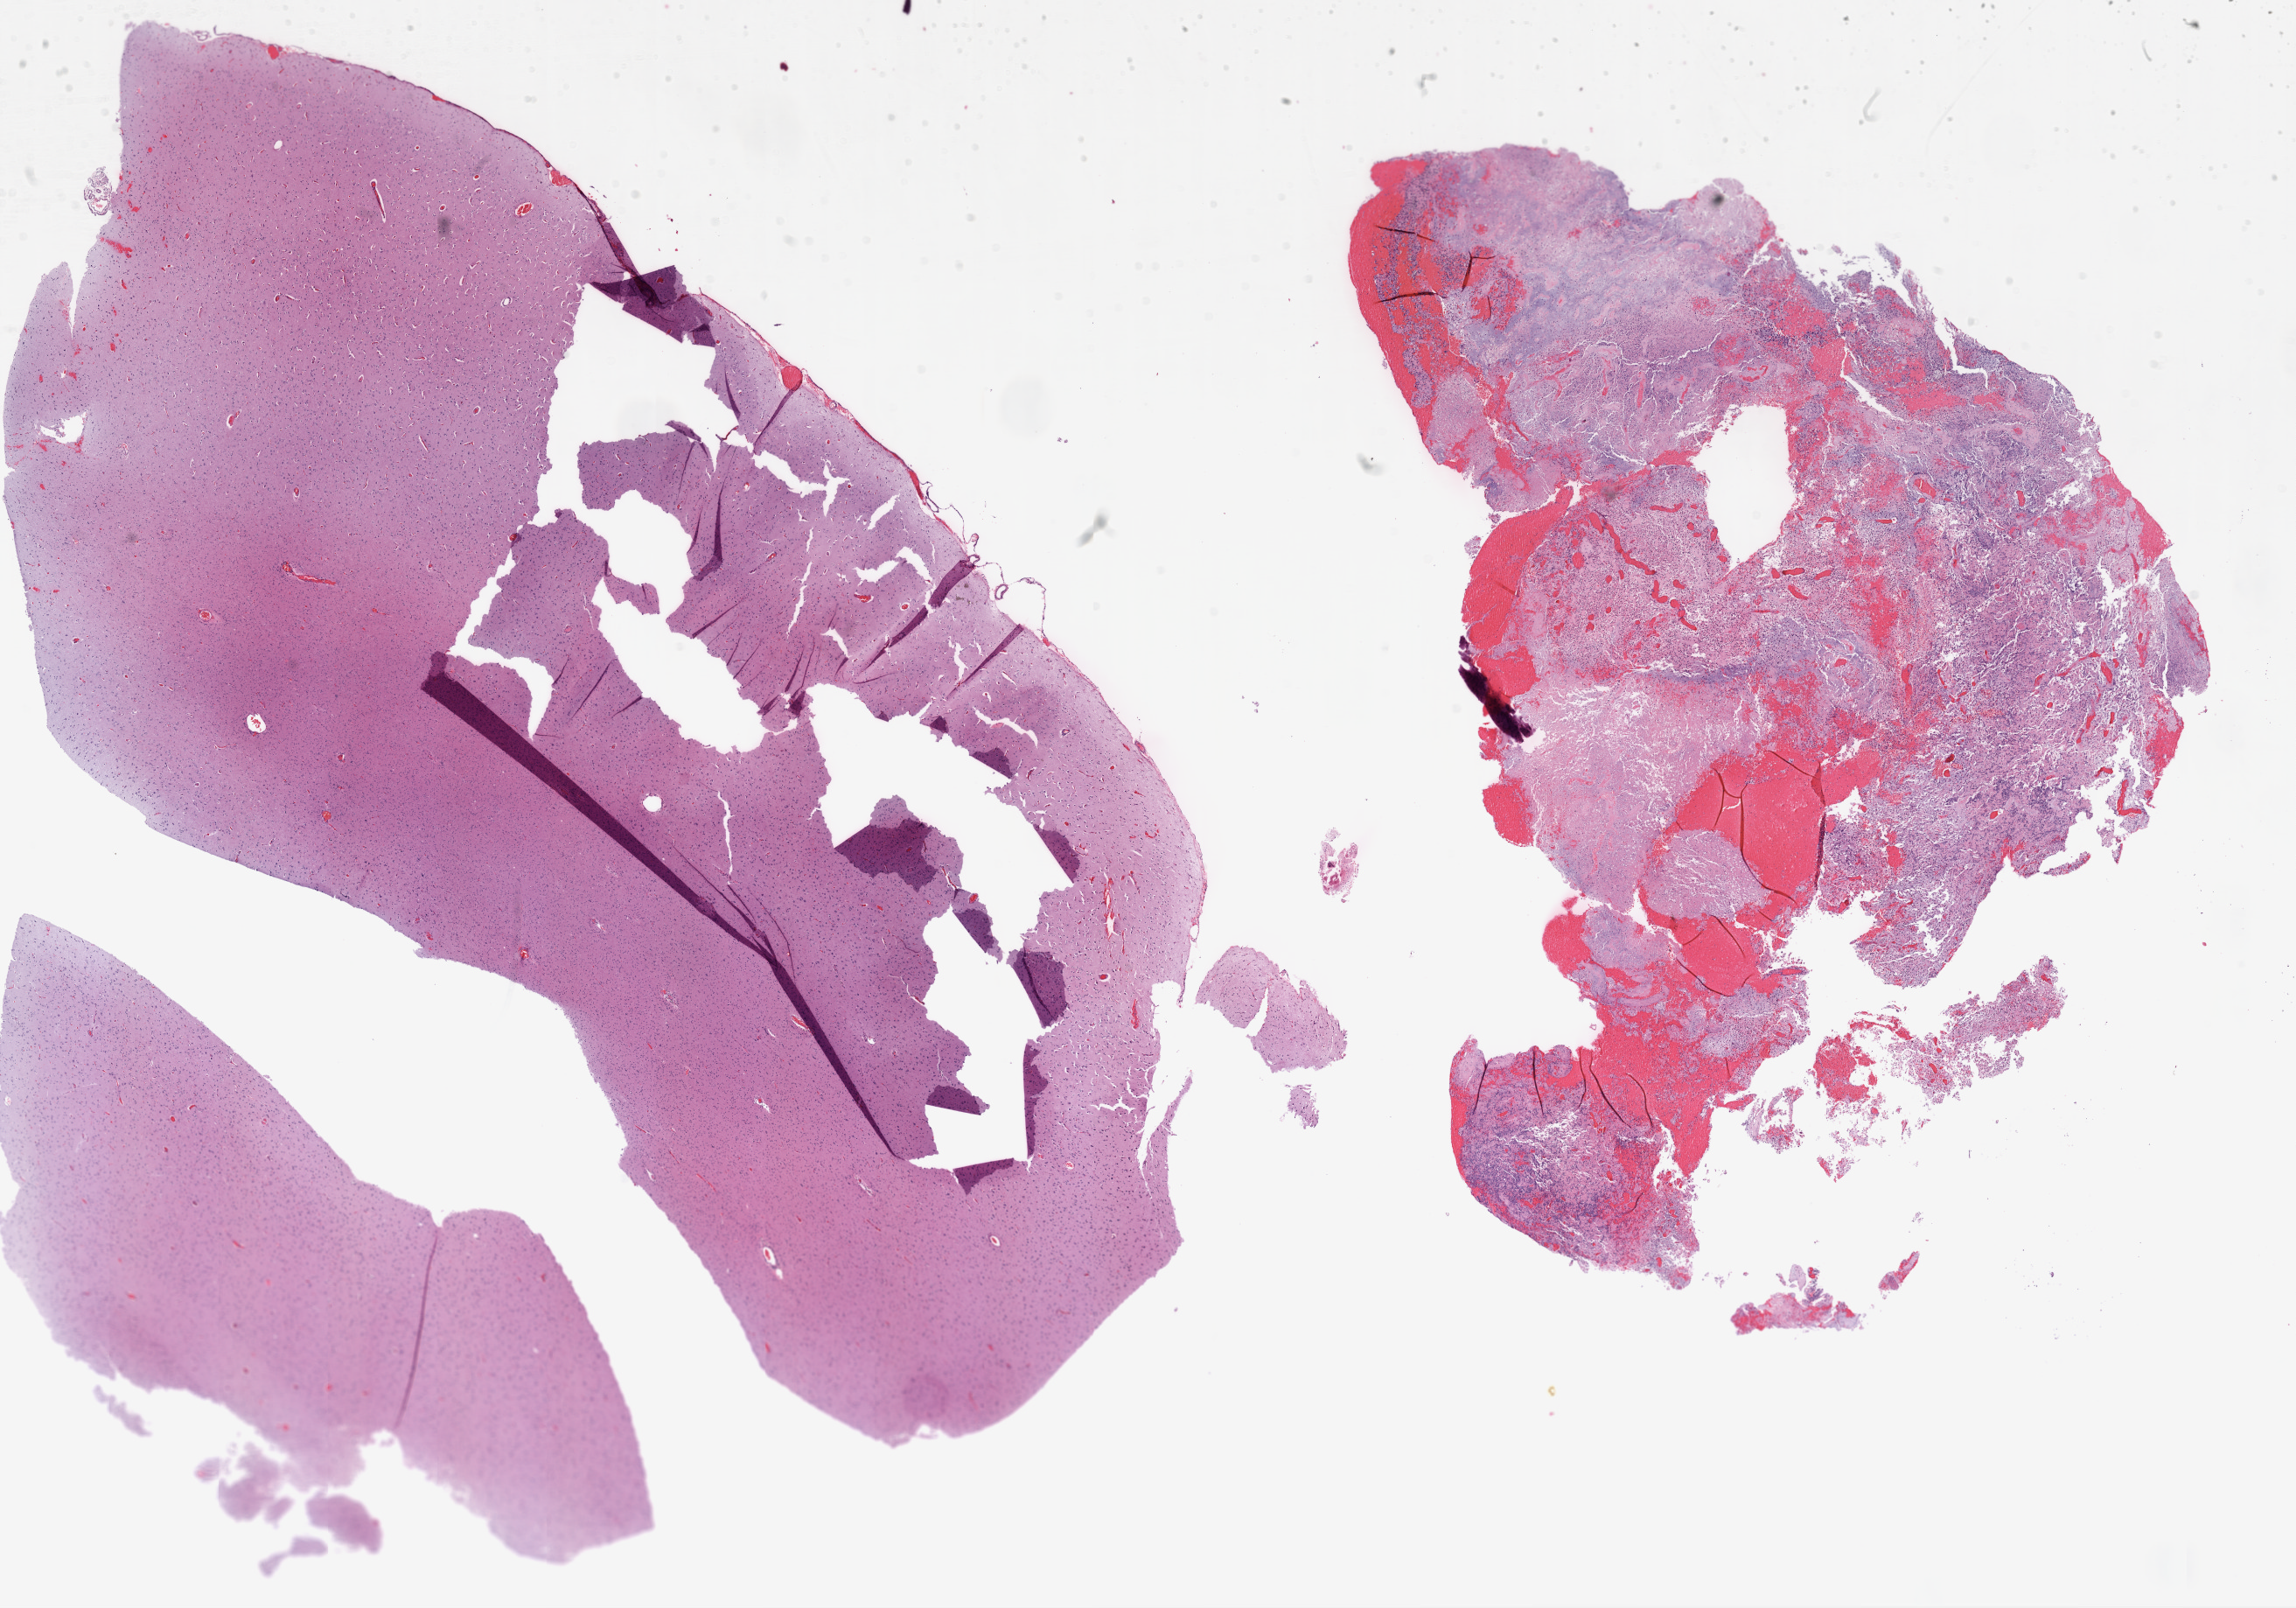
Whole-slide histology image, Hematoxylin and eosin (H&E) stained — shown as a low-resolution overview of the whole scanned area (about 21.1 x 14.7 mm, from a 20x scan). Formalin-fixed paraffin-embedded (FFPE) diagnostic section. Primary tumour sample from the brain. Male, age 57 years at initial diagnosis.
Pathologic diagnosis: Glioblastoma.